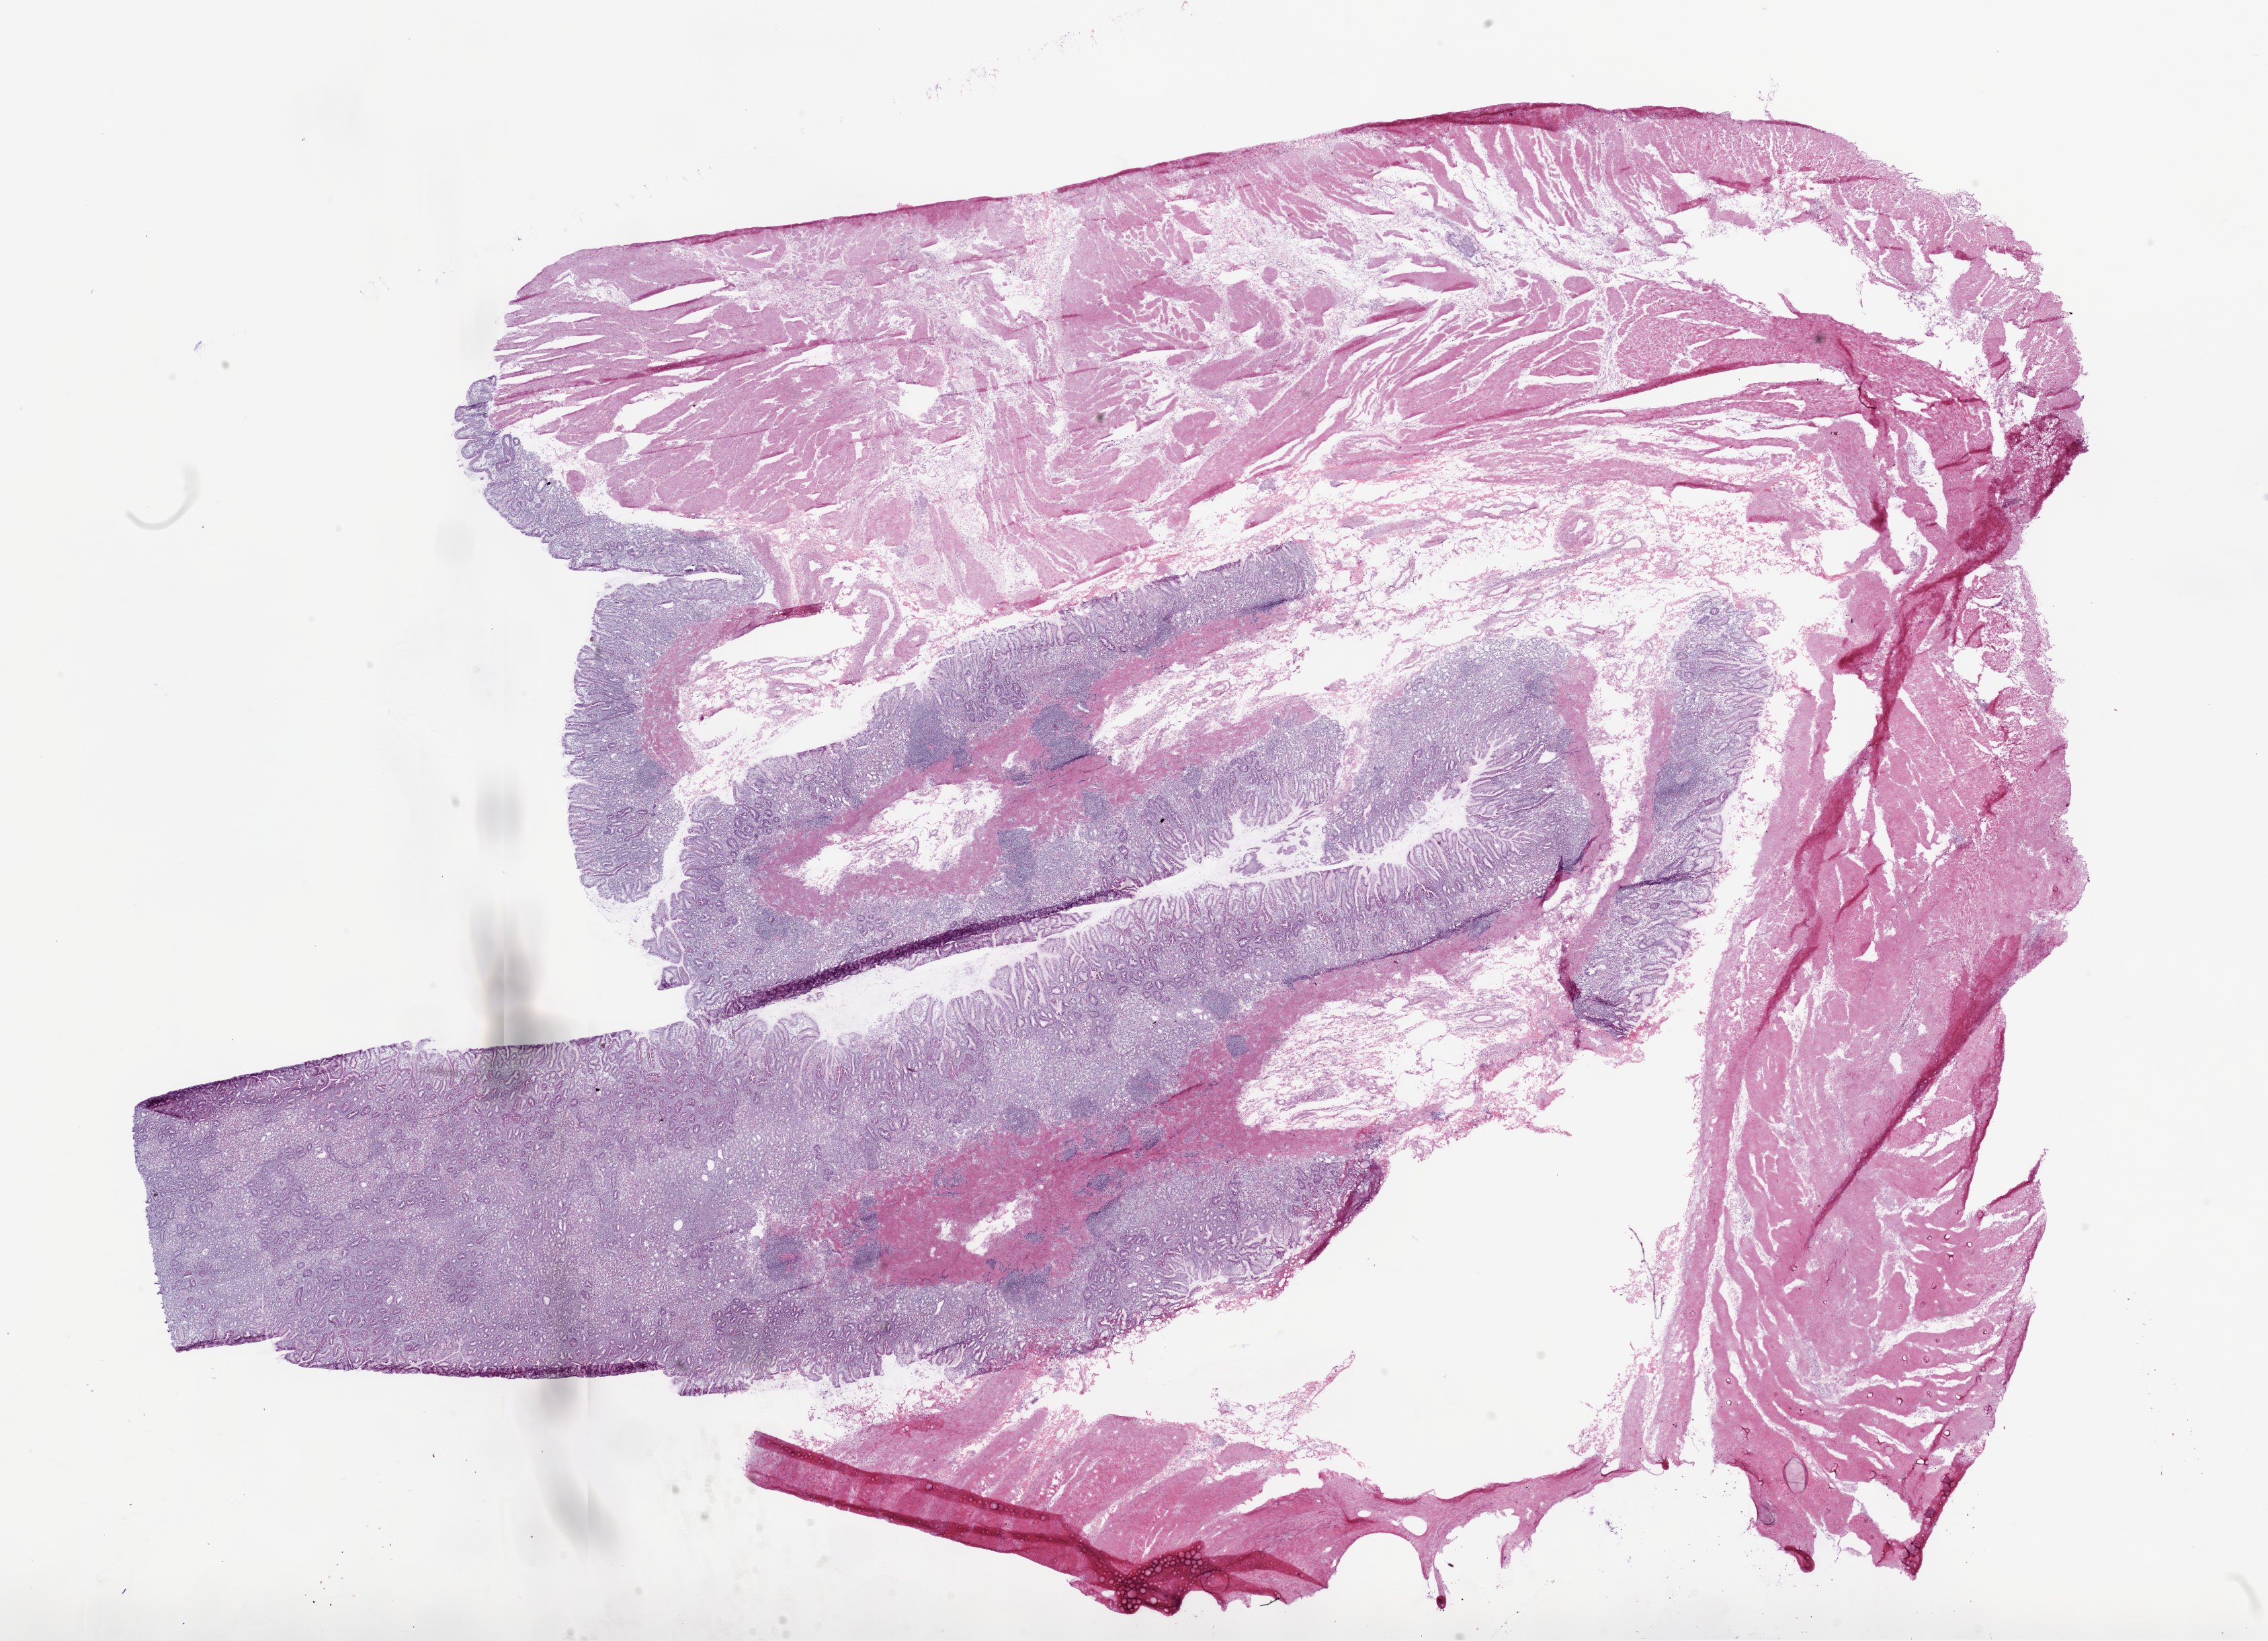
H&E-stained whole-slide image, low-resolution overview of the scanned area, about 27.1 x 19.6 mm (acquisition: 20x scan). Frozen section. Solid tissue normal (non-tumour tissue) sample from the stomach. Patient: male, age at initial diagnosis 78 years.
* this section: solid tissue normal sample (biorepository sample class)
* patient diagnosis: Adenocarcinoma, NOS